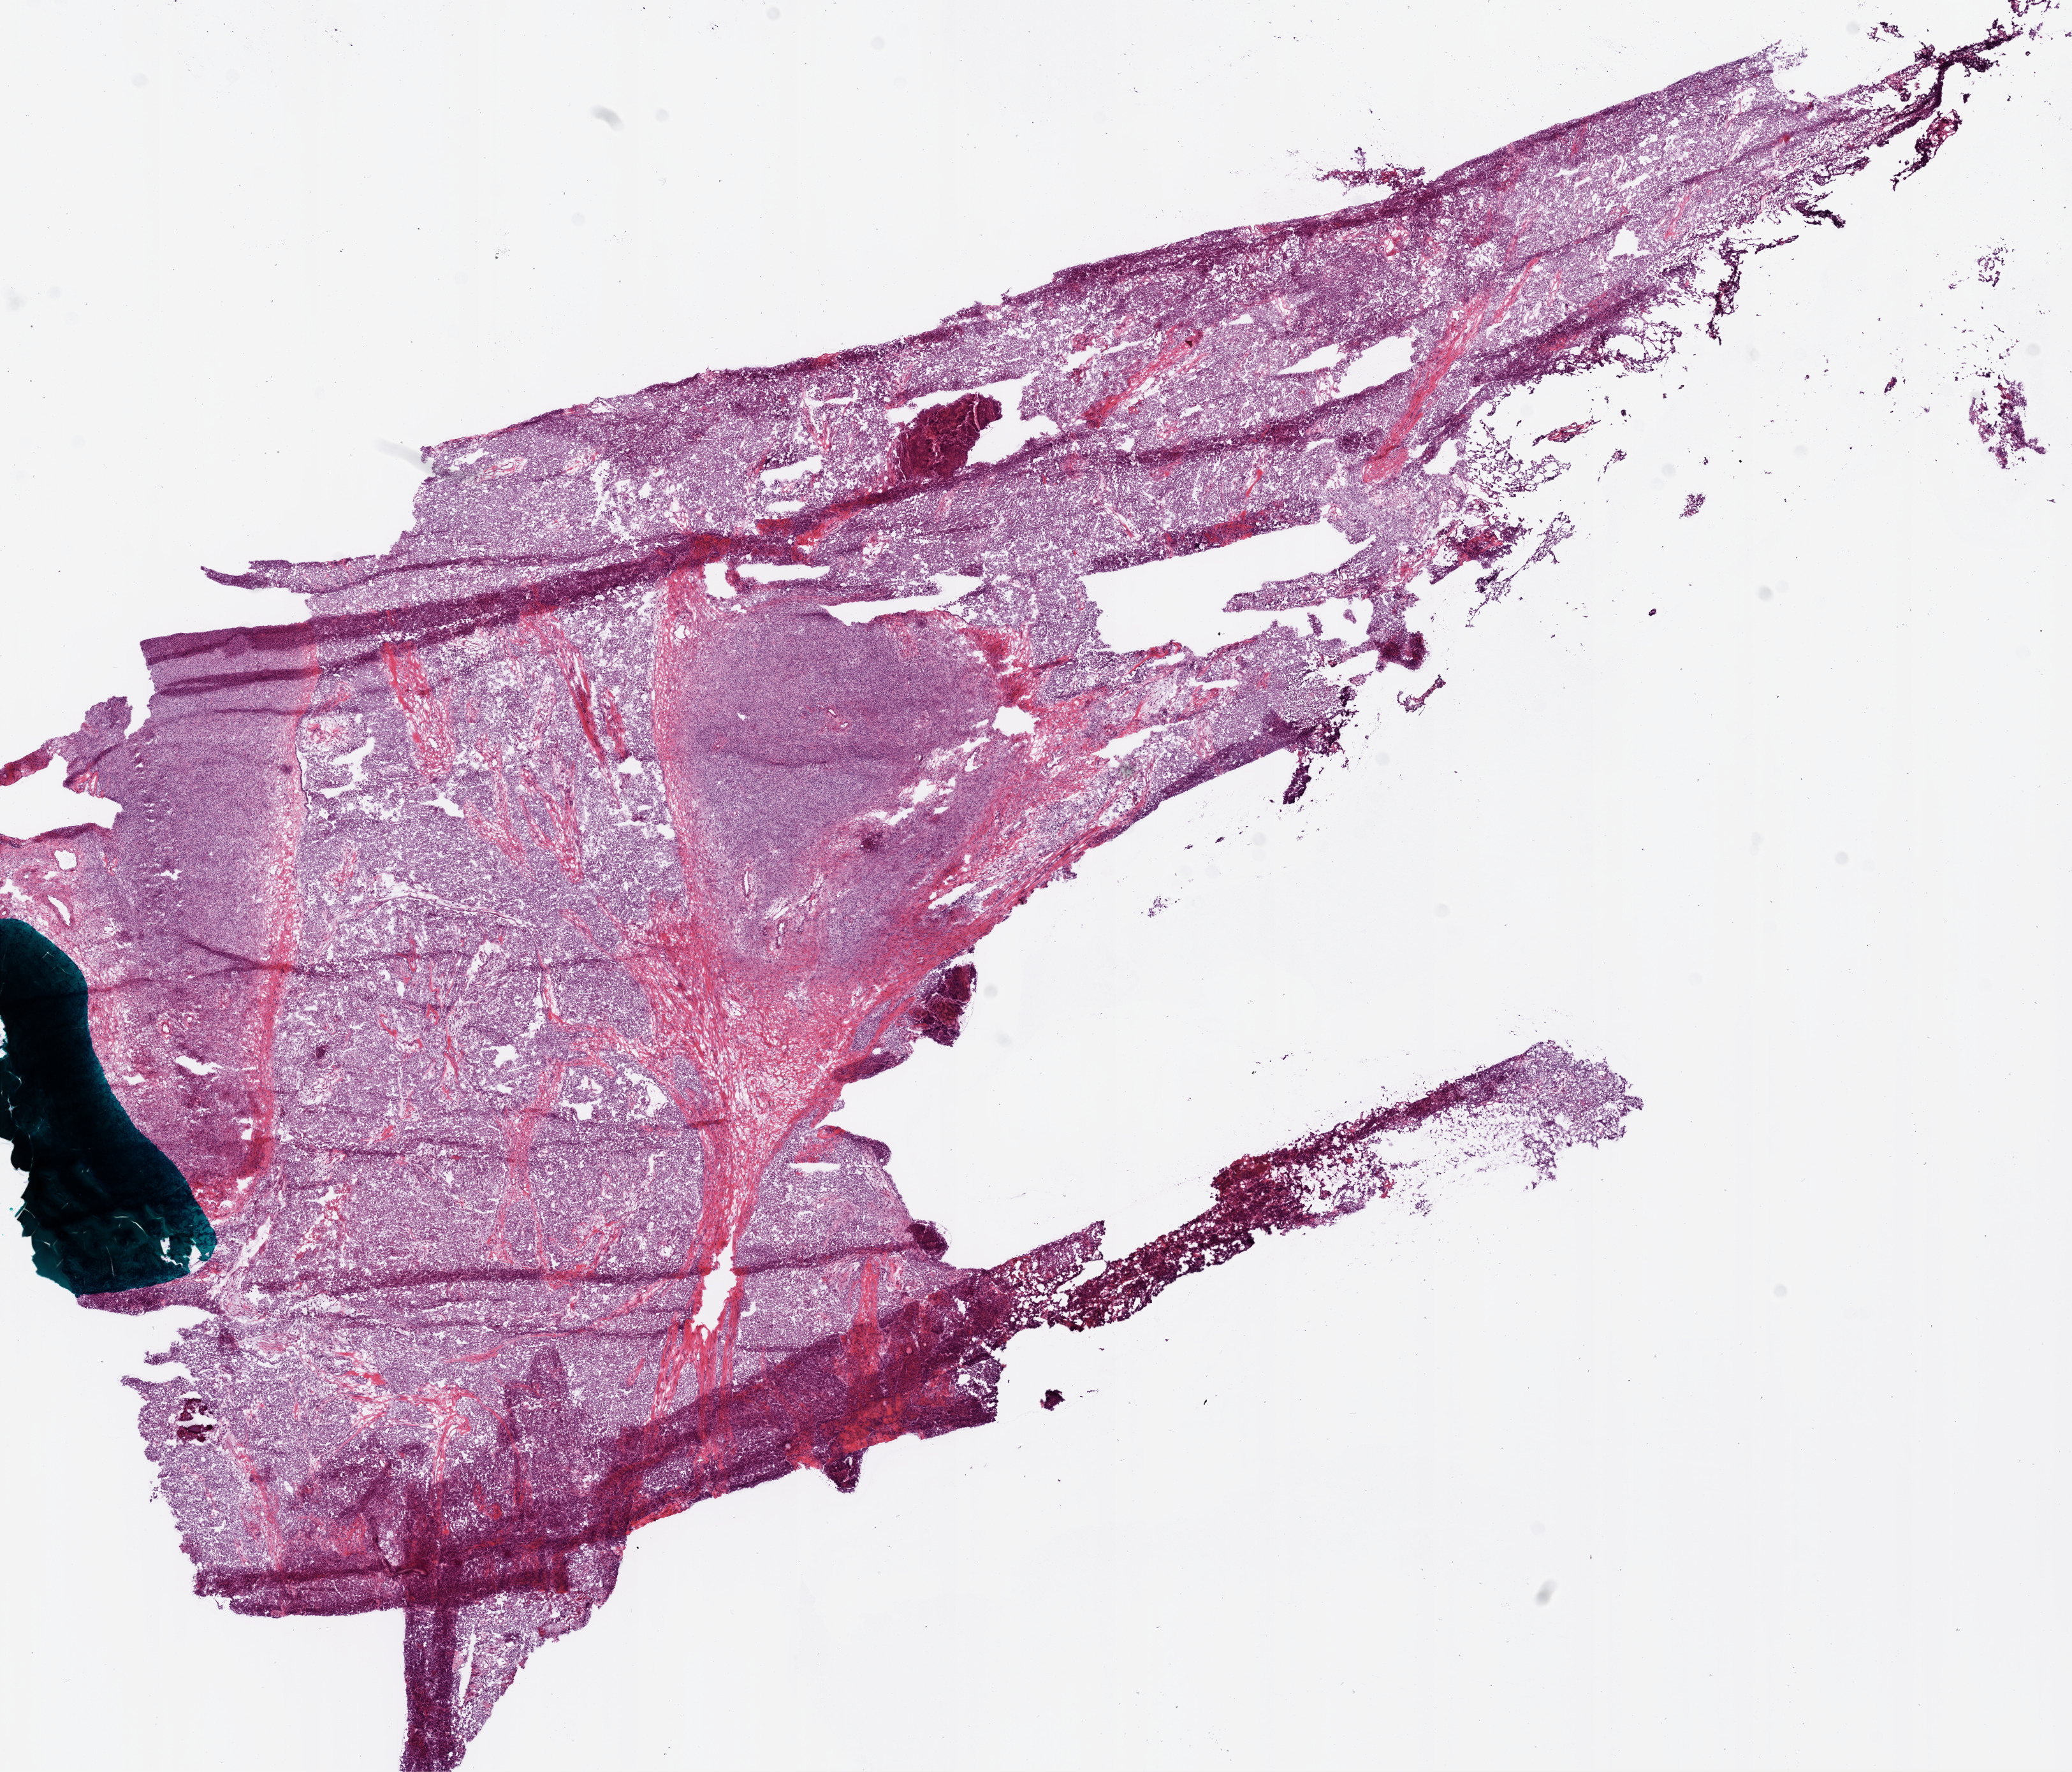
Hematoxylin and eosin (H&E) stained whole-slide image — low-resolution overview of the scanned area, about 13.0 x 11.2 mm (acquisition: 20x scan). Frozen section from the bottom of the tissue portion. Ovary, primary tumour sample. Patient: female, age at initial diagnosis 61 years. Histologic grade: G3 (poorly differentiated). Pathologist review of this section (percent, as recorded): tumour cells 60%, tumour nuclei 95%, normal cells 30%, stromal cells 0%, necrosis 10%.
* diagnosis: Serous cystadenocarcinoma, NOS
* FIGO stage: IIIC